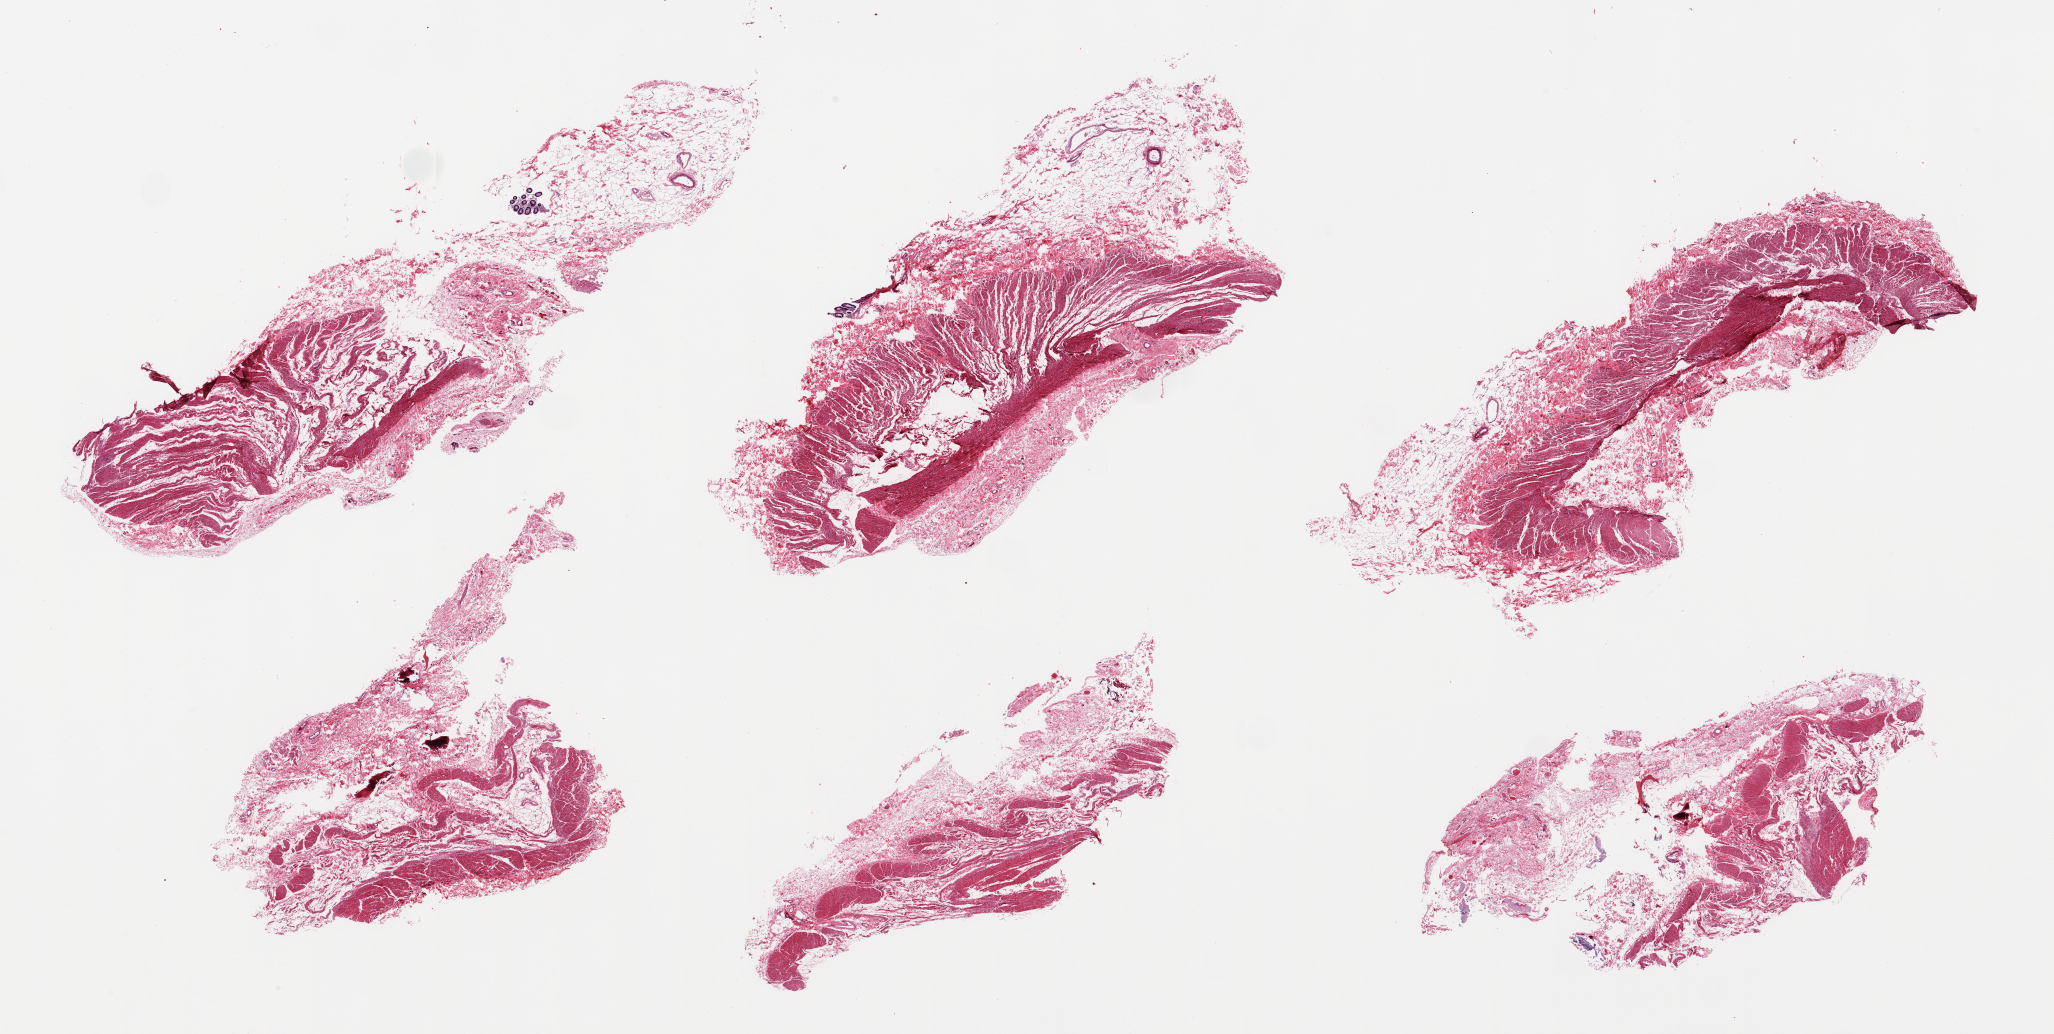
Digitized haematoxylin and eosin-stained section, brightfield, whole scanned area (about 32.5 x 16.4 mm) shown as a low-resolution overview; PAXgene-fixed paraffin-embedded (PFPE) section; target tissue: sigmoid colon; donor tissue sample. Donor: male.
Pathologist's review note for this sample: 6 pieces; ~50% muscularis, ~50% submucosa/serosa, fragments of bone.